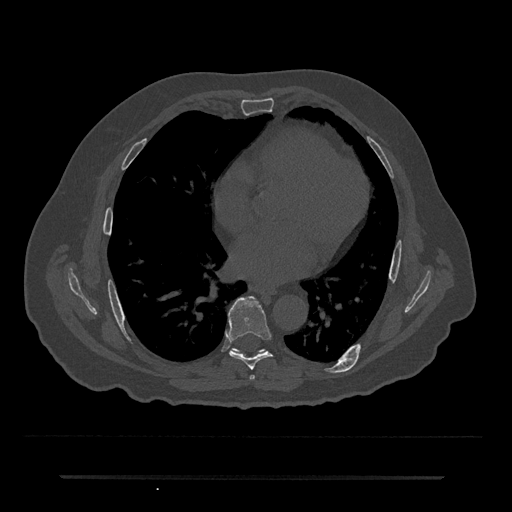
CT including the spine, one axial slice. Position 374 of 797 along the scan axis. Reconstruction kernel Br40s/3. Bone window (W 1800 / L 400 HU). 0.5 mm slice thickness. 512 × 512 image matrix, field of view 437 × 437 mm. Patient: male, 69 years. Case-level facts recorded for this patient, not image findings: primary cancer: prostate.
Structures marked on this image (semi-automatically segmented with operator editing):
- T6 vertebra: bounding box (x1, y1, x2, y2) in pixels: (249, 375, 255, 380)
- T7 vertebra: (228, 296, 272, 370)
- T8 vertebra: (233, 349, 263, 353)